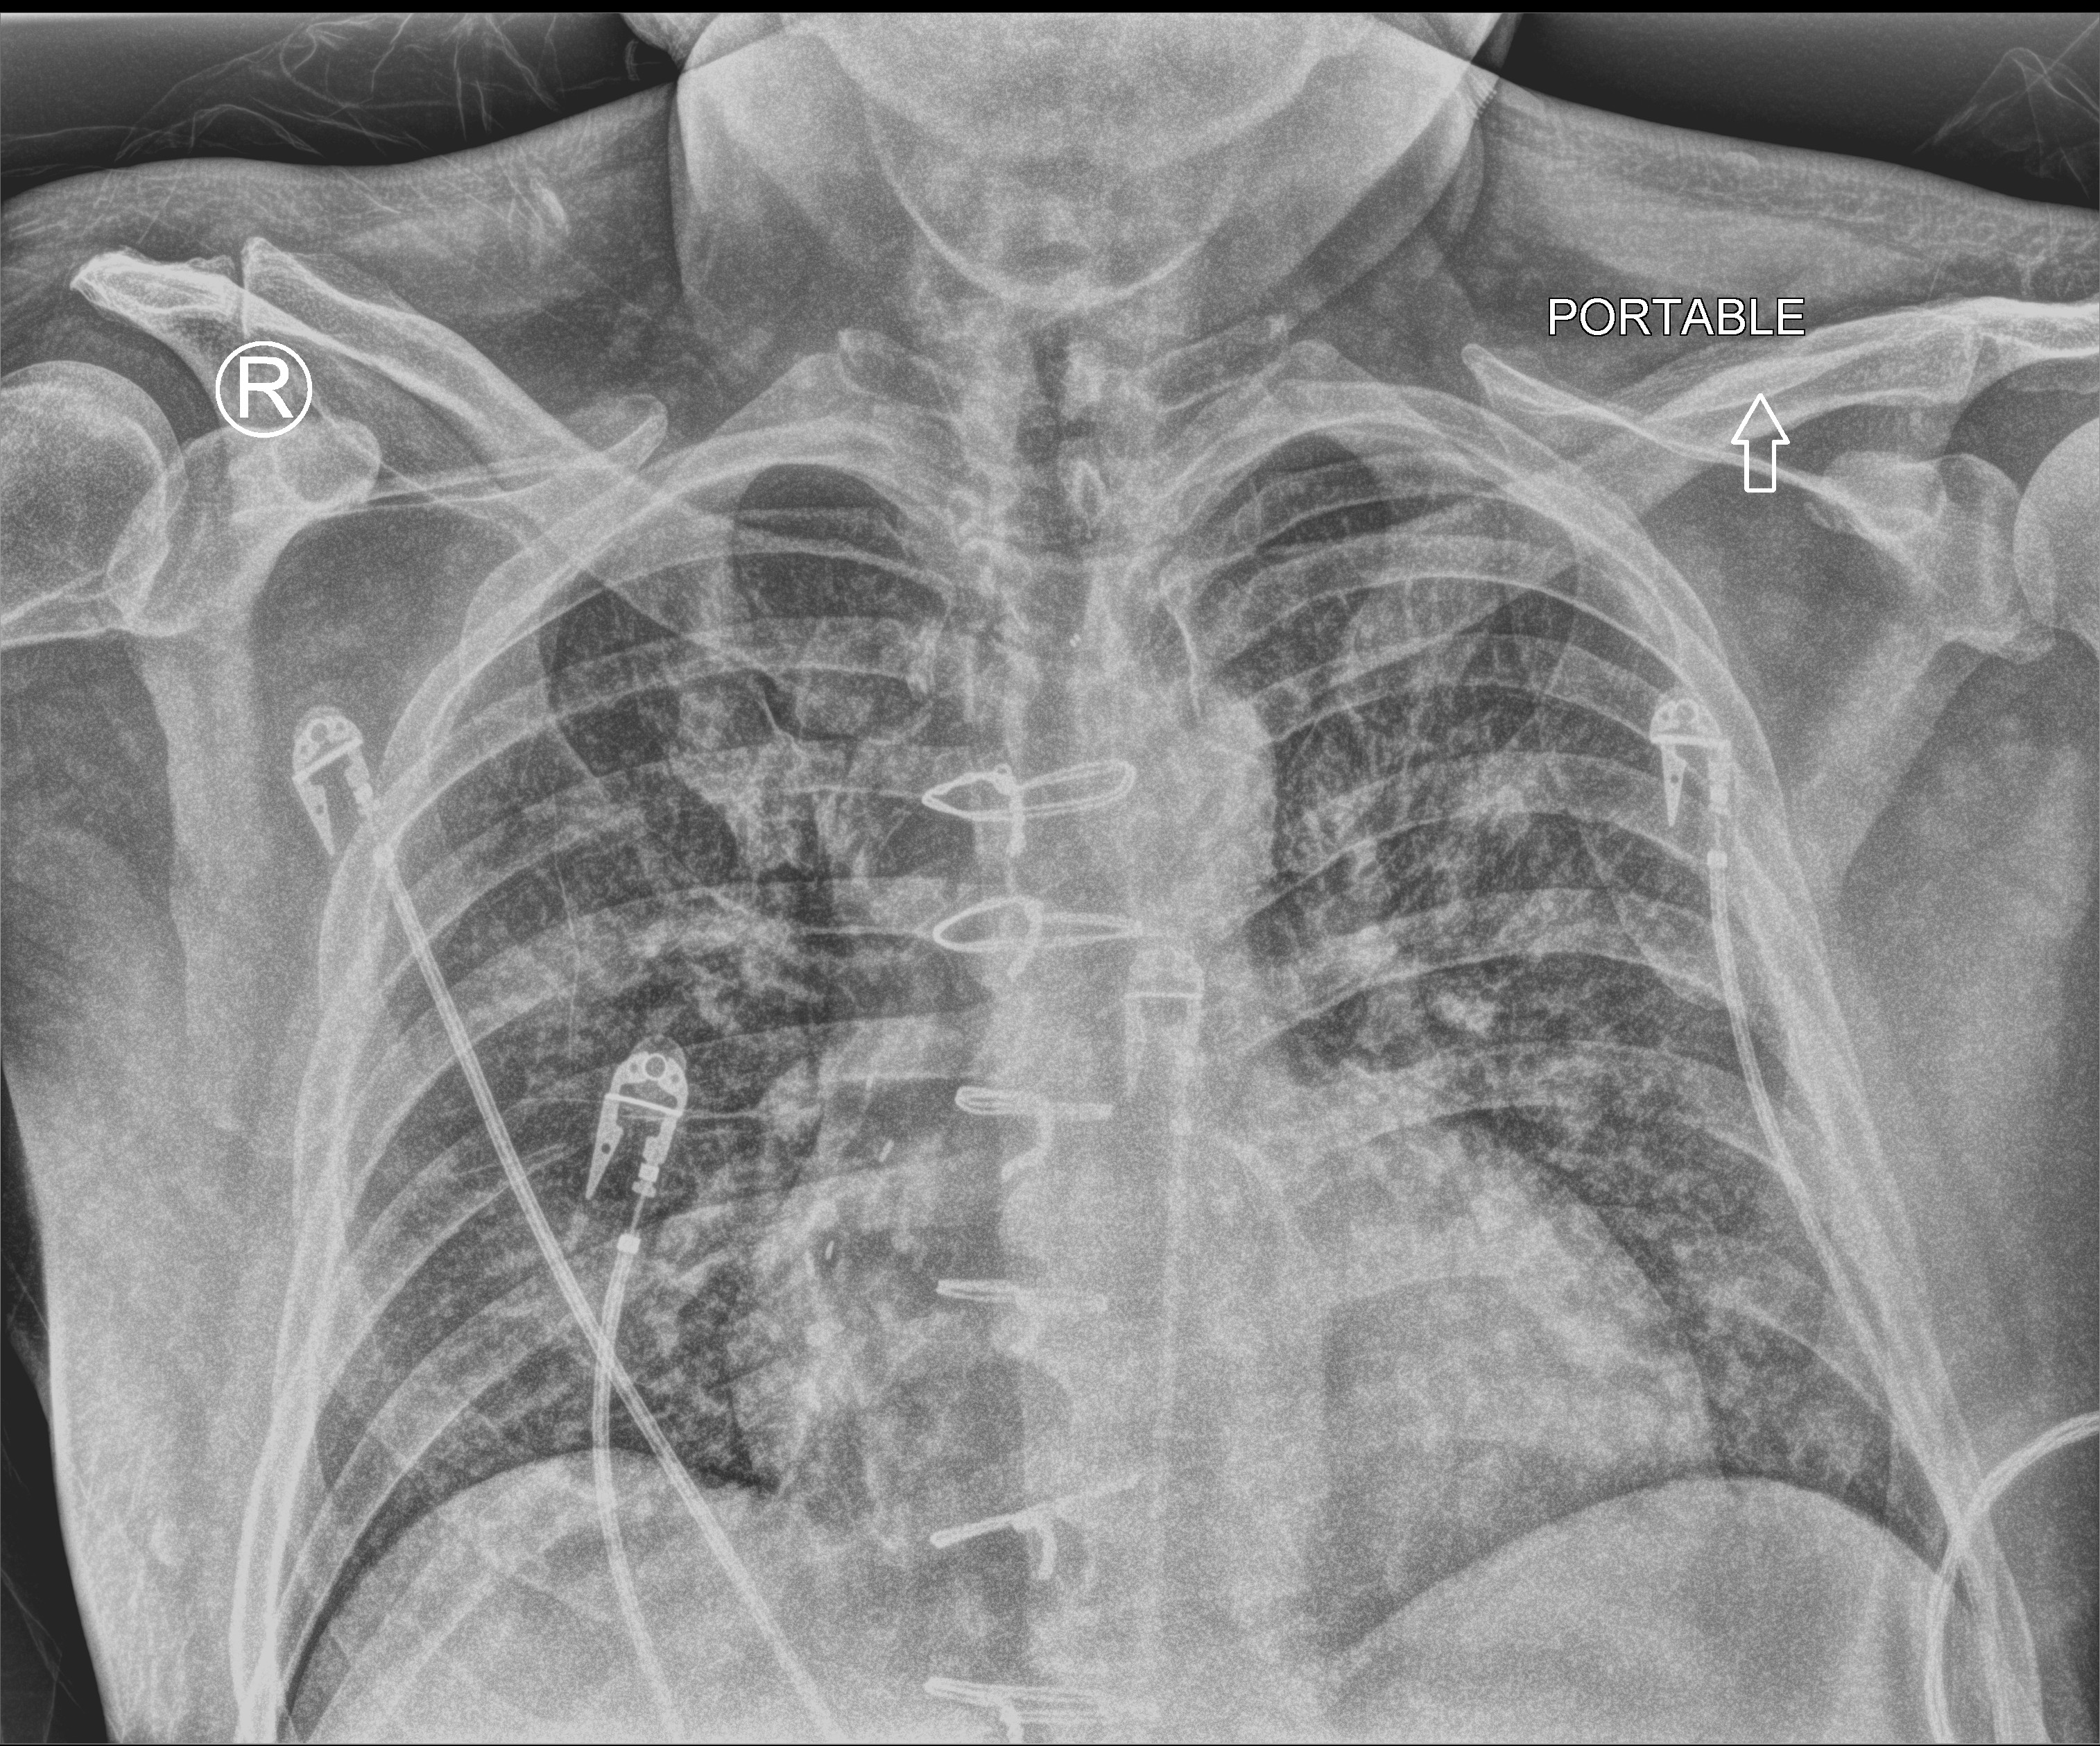
Chest X-ray (portable). Adult patient hospitalised with COVID-19, age 18–59 years.
Admission-level facts for this patient (not findings on this image; timing relative to this image not recorded):
- other chronic lung disease (admission record): no